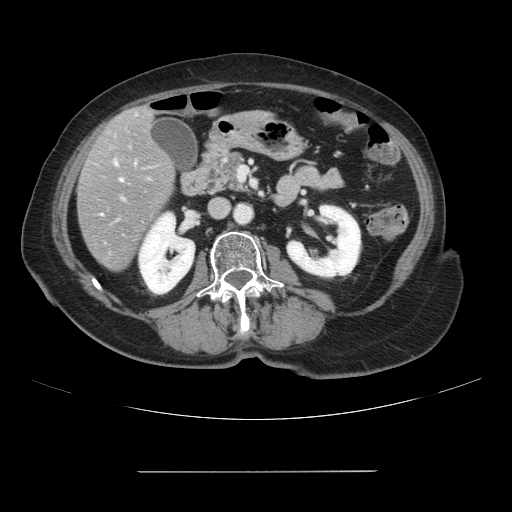
Contrast-enhanced abdominal CT, one axial slice. Position 29 of 111 along the scan axis. 120 kVp. Intravenous contrast given. Soft-tissue window (W 400 / L 40 HU). 2.5 mm slice thickness. 512 × 512 image matrix, field of view 400 × 400 mm. Female patient, age 74 years. From the clinical record (not read from this slice): diagnosis: colorectal cancer liver metastases, imaged before liver resection; multiple liver metastases: yes; largest metastasis: 1.1 cm.
Outlined on this slice (expert manual segmentation):
- hepatic veins: bounding box (x1, y1, x2, y2) in pixels: (115, 162, 122, 181)
- liver: (78, 107, 174, 271)
- planned liver remnant (the part of the liver to remain after resection): (142, 108, 154, 120)